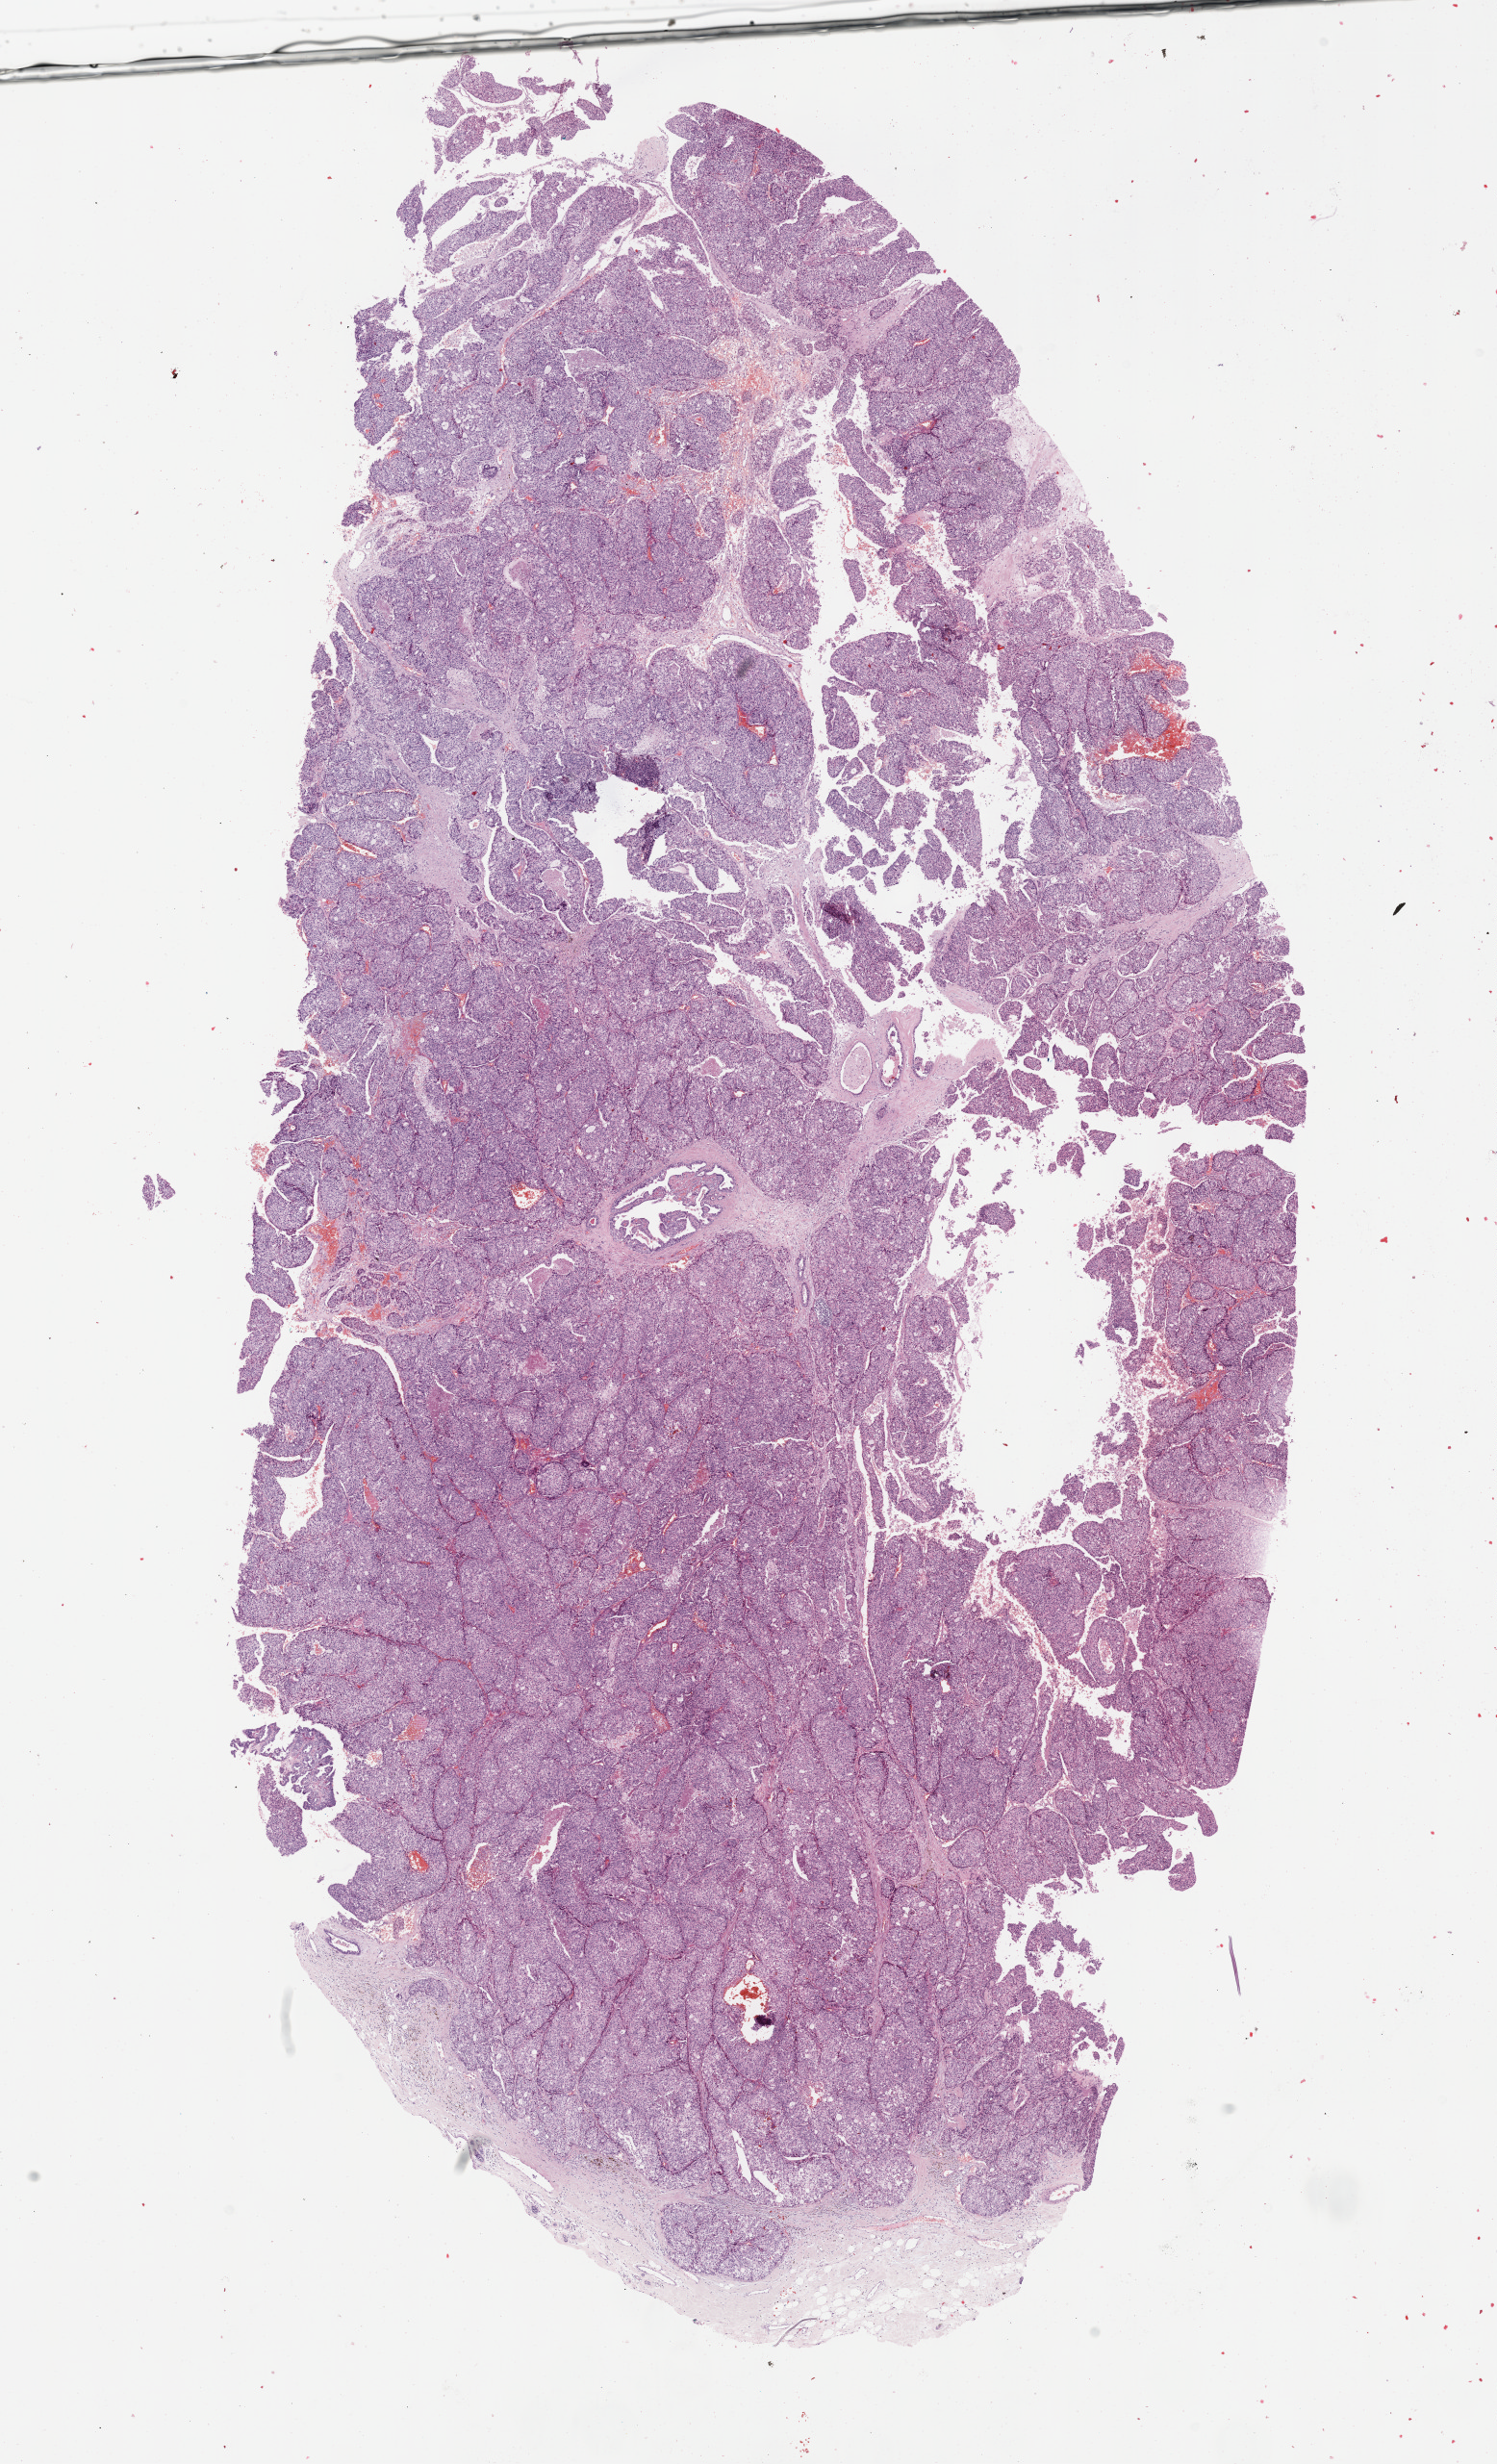
Whole-slide histology image, H&E-stained — a low-resolution overview of the entire scanned area, about 12.6 x 20.7 mm (from a 40x scan). Formalin-fixed paraffin-embedded (FFPE) diagnostic section. Sample: primary tumour, breast. Female, age 70 years at initial diagnosis.
- lymph nodes positive (case pathology): 0 of 15 examined
- TNM: T2 N0 M0
- AJCC pathologic stage: IIA (7th edition)
- pathologic diagnosis: Infiltrating duct mixed with other types of carcinoma
- laterality: left